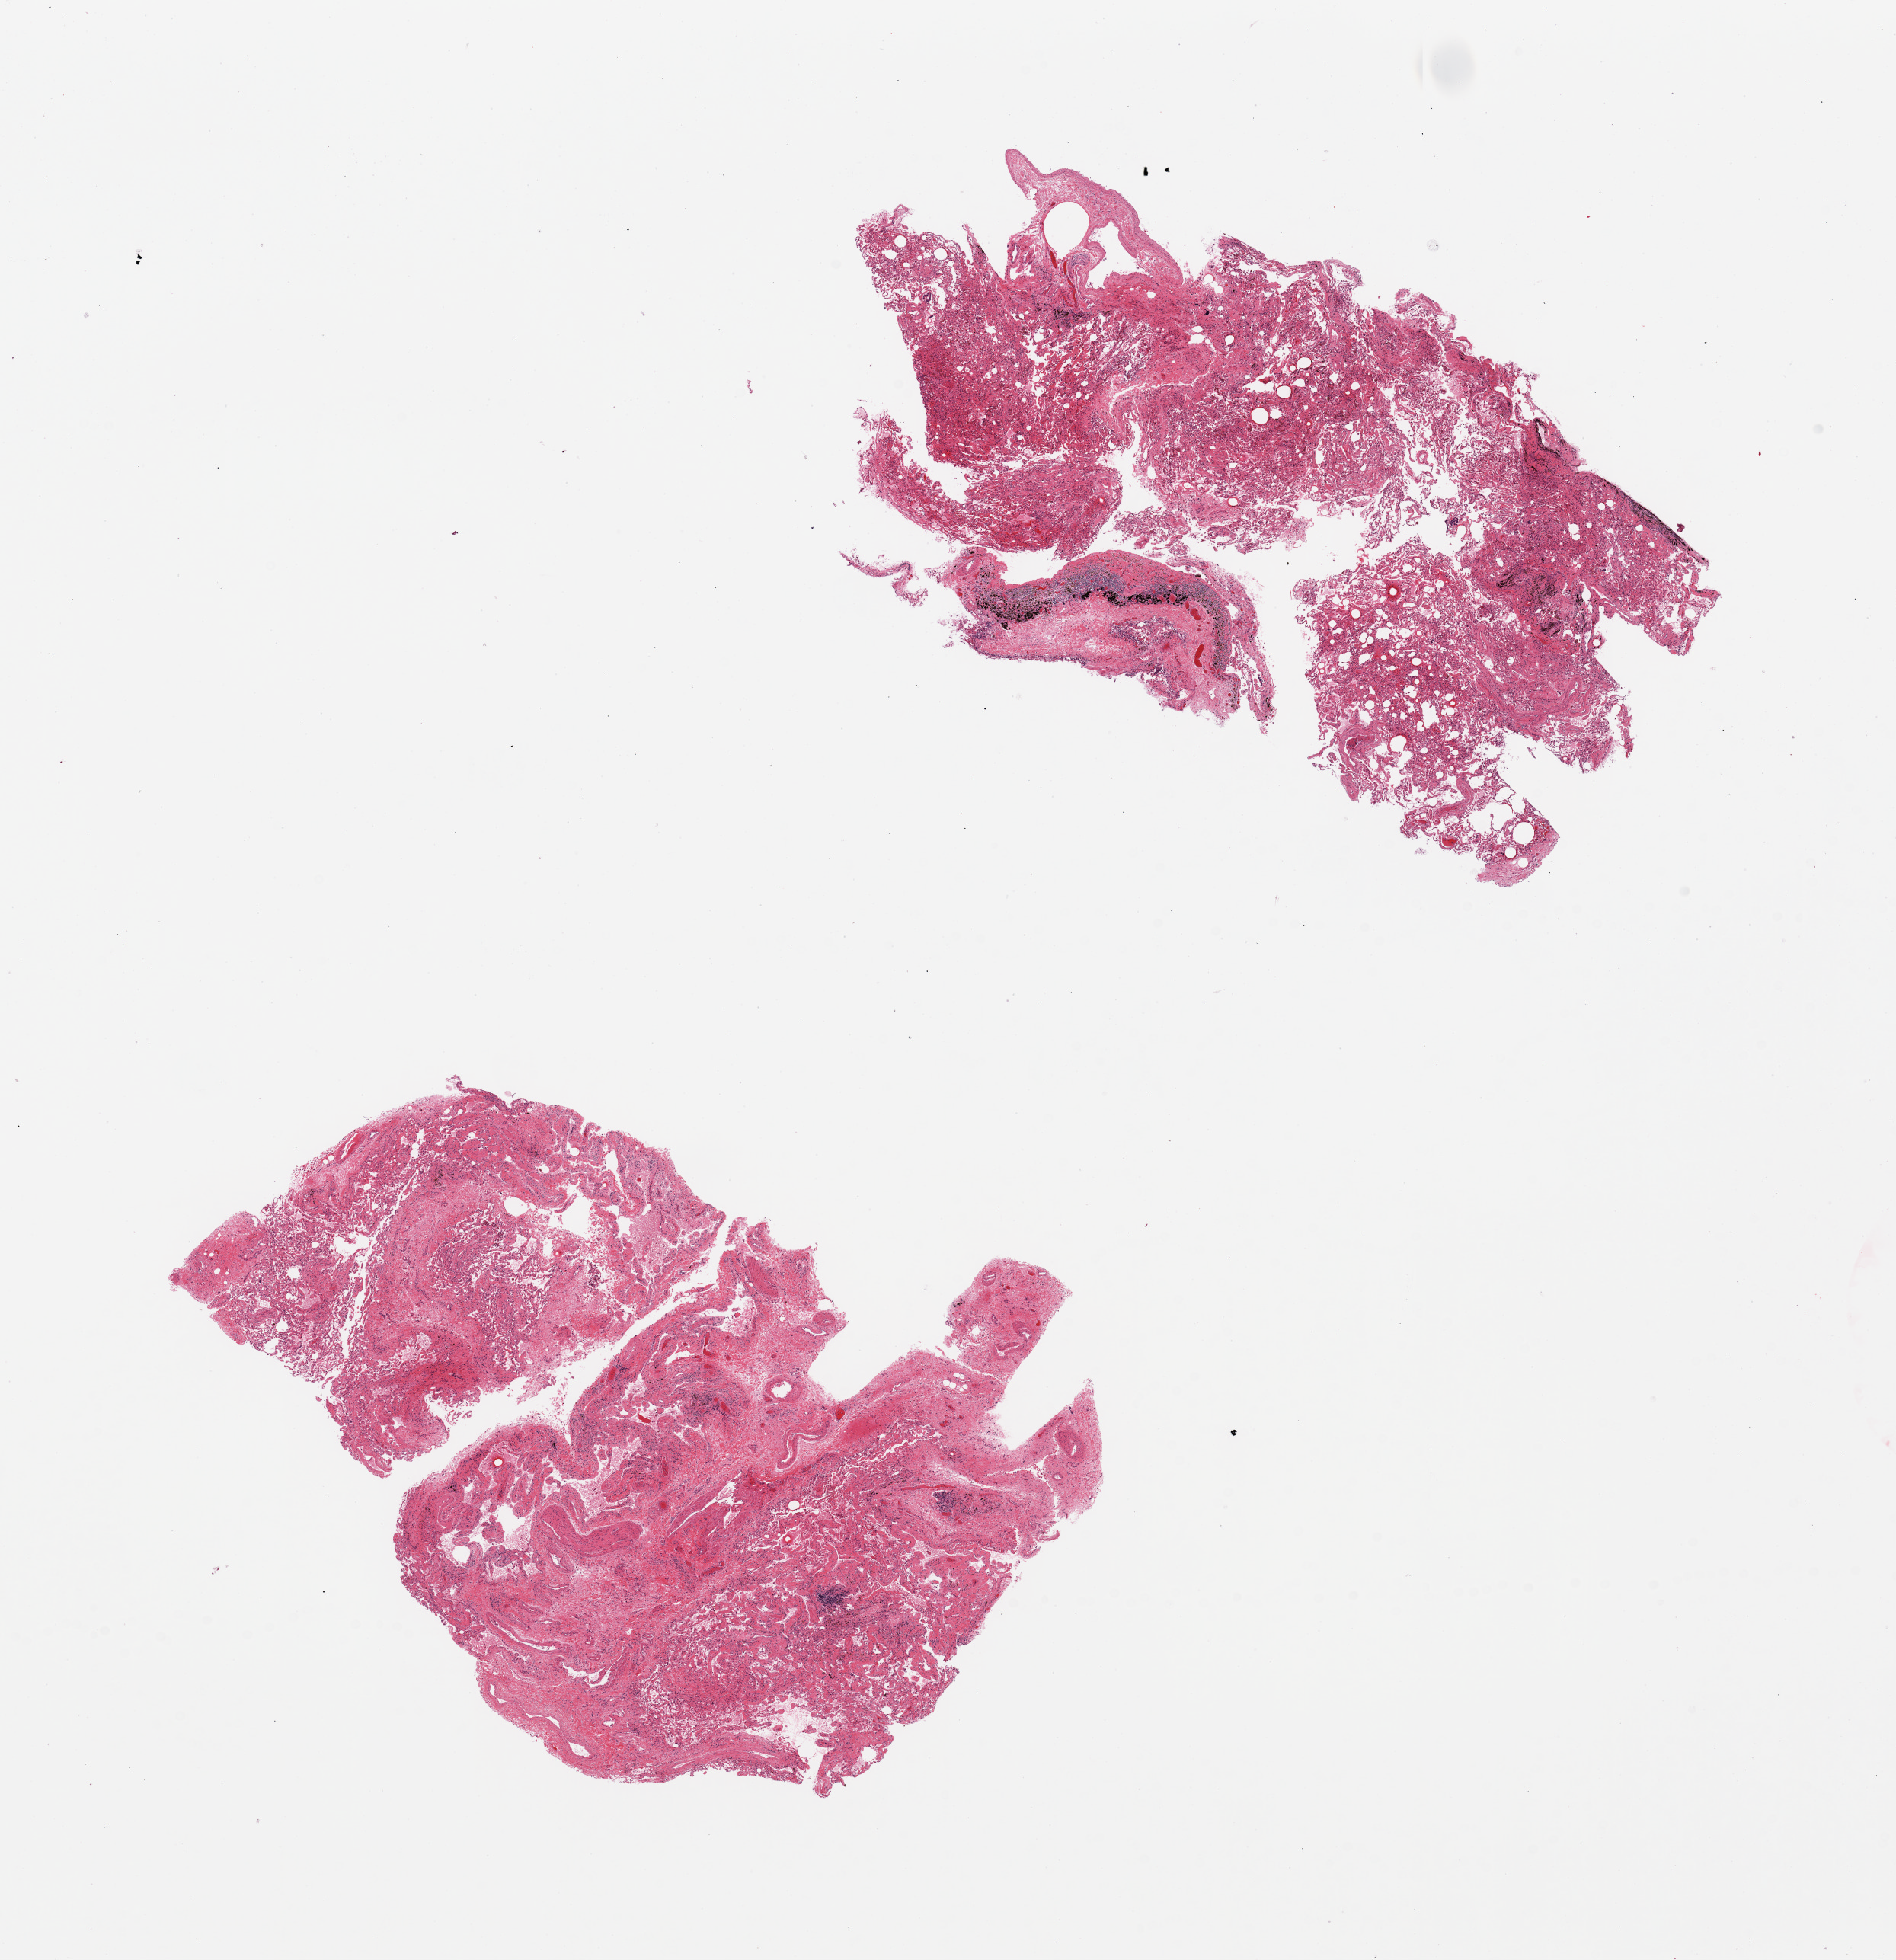
Digitized hematoxylin and eosin (H&E)-stained section, a low-resolution overview of the entire scanned area, about 19.7 x 20.4 mm, PAXgene-fixed paraffin-embedded (PFPE) section, target tissue: lung, tissue donor sample. Donor: female.
- review note (as recorded): 2 pieces, marked congestion/interstitial fibrosis; Prominent anthracotic pigment deposition